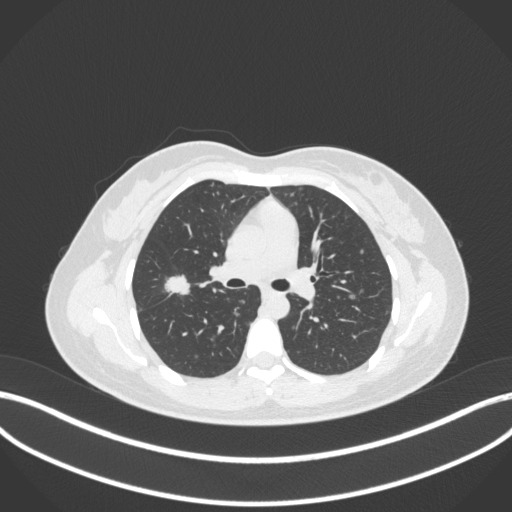
Chest CT, one axial slice. Slice 203 of 214 in the series (ordered by position). Reconstruction kernel B31f. 120 kVp. Lung window (W 1500 / L -600 HU). 1 mm slice thickness. 512 × 512 image matrix, field of view 400 × 400 mm. Female patient, age 33 years. From the clinical record (not read from this slice): clinical TNM (as recorded): T1c N0 M0.
Annotated regions visible in this slice (rectangle marked by the reading radiologist):
- lung tumour (recorded histology: adenocarcinoma): bounding box (x1, y1, x2, y2) in pixels: (163, 272, 197, 303)